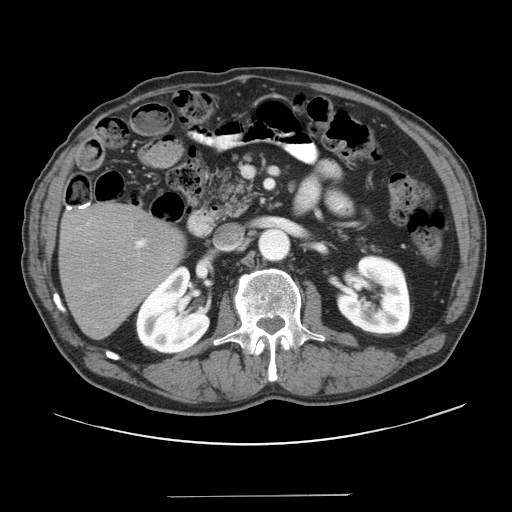
Contrast-enhanced abdominal CT, one axial slice; position 15 of 41 along the scan axis; reconstruction kernel STANDARD; 120 kVp; intravenous contrast given; soft-tissue window (W 400 / L 40 HU); 512 × 512 image matrix. Male patient, age 75 years. From the clinical record (not read from this slice): diagnosis: colorectal cancer liver metastases, imaged before liver resection; multiple liver metastases: no; largest metastasis: 5.2 cm; chemotherapy before resection: no.
Annotated regions visible in this slice (manually delineated by an expert):
- liver: box from (x=60, y=206) to (x=182, y=339) px
- planned liver remnant (the part of the liver to remain after resection): (x=60, y=206)–(x=182, y=338)
- portal vein (with intrahepatic branches): (x=135, y=239)–(x=147, y=249)